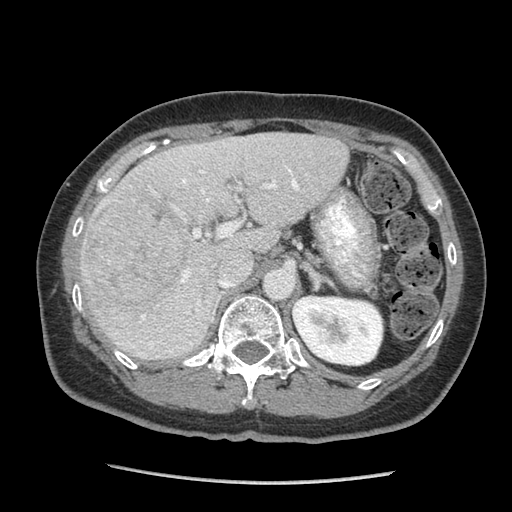
Contrast-enhanced abdominal CT (liver protocol), one axial slice; position 53 of 105 along the scan axis; soft-tissue window (W 400 / L 40 HU); 2.5 mm slice thickness; 512 × 512 image matrix. Case-level facts recorded for this patient, not image findings: diagnosis: hepatocellular carcinoma (patient treated with transarterial chemoembolisation; whether this scan precedes or follows treatment is not stated here); TNM stage (as recorded): Stage-I; Child-Pugh class: A; tumour nodularity: uninodular.
Outlined on this slice (semi-automatic segmentation, software-assisted and operator-edited):
- liver parenchyma outside the tumour (the mass and vessels are separate outlines, so this box may not span the whole liver): bounding box [x1, y1, x2, y2] px = [80, 132, 348, 360]
- mass: [83, 195, 197, 308]
- liver vessels: [117, 162, 299, 354]